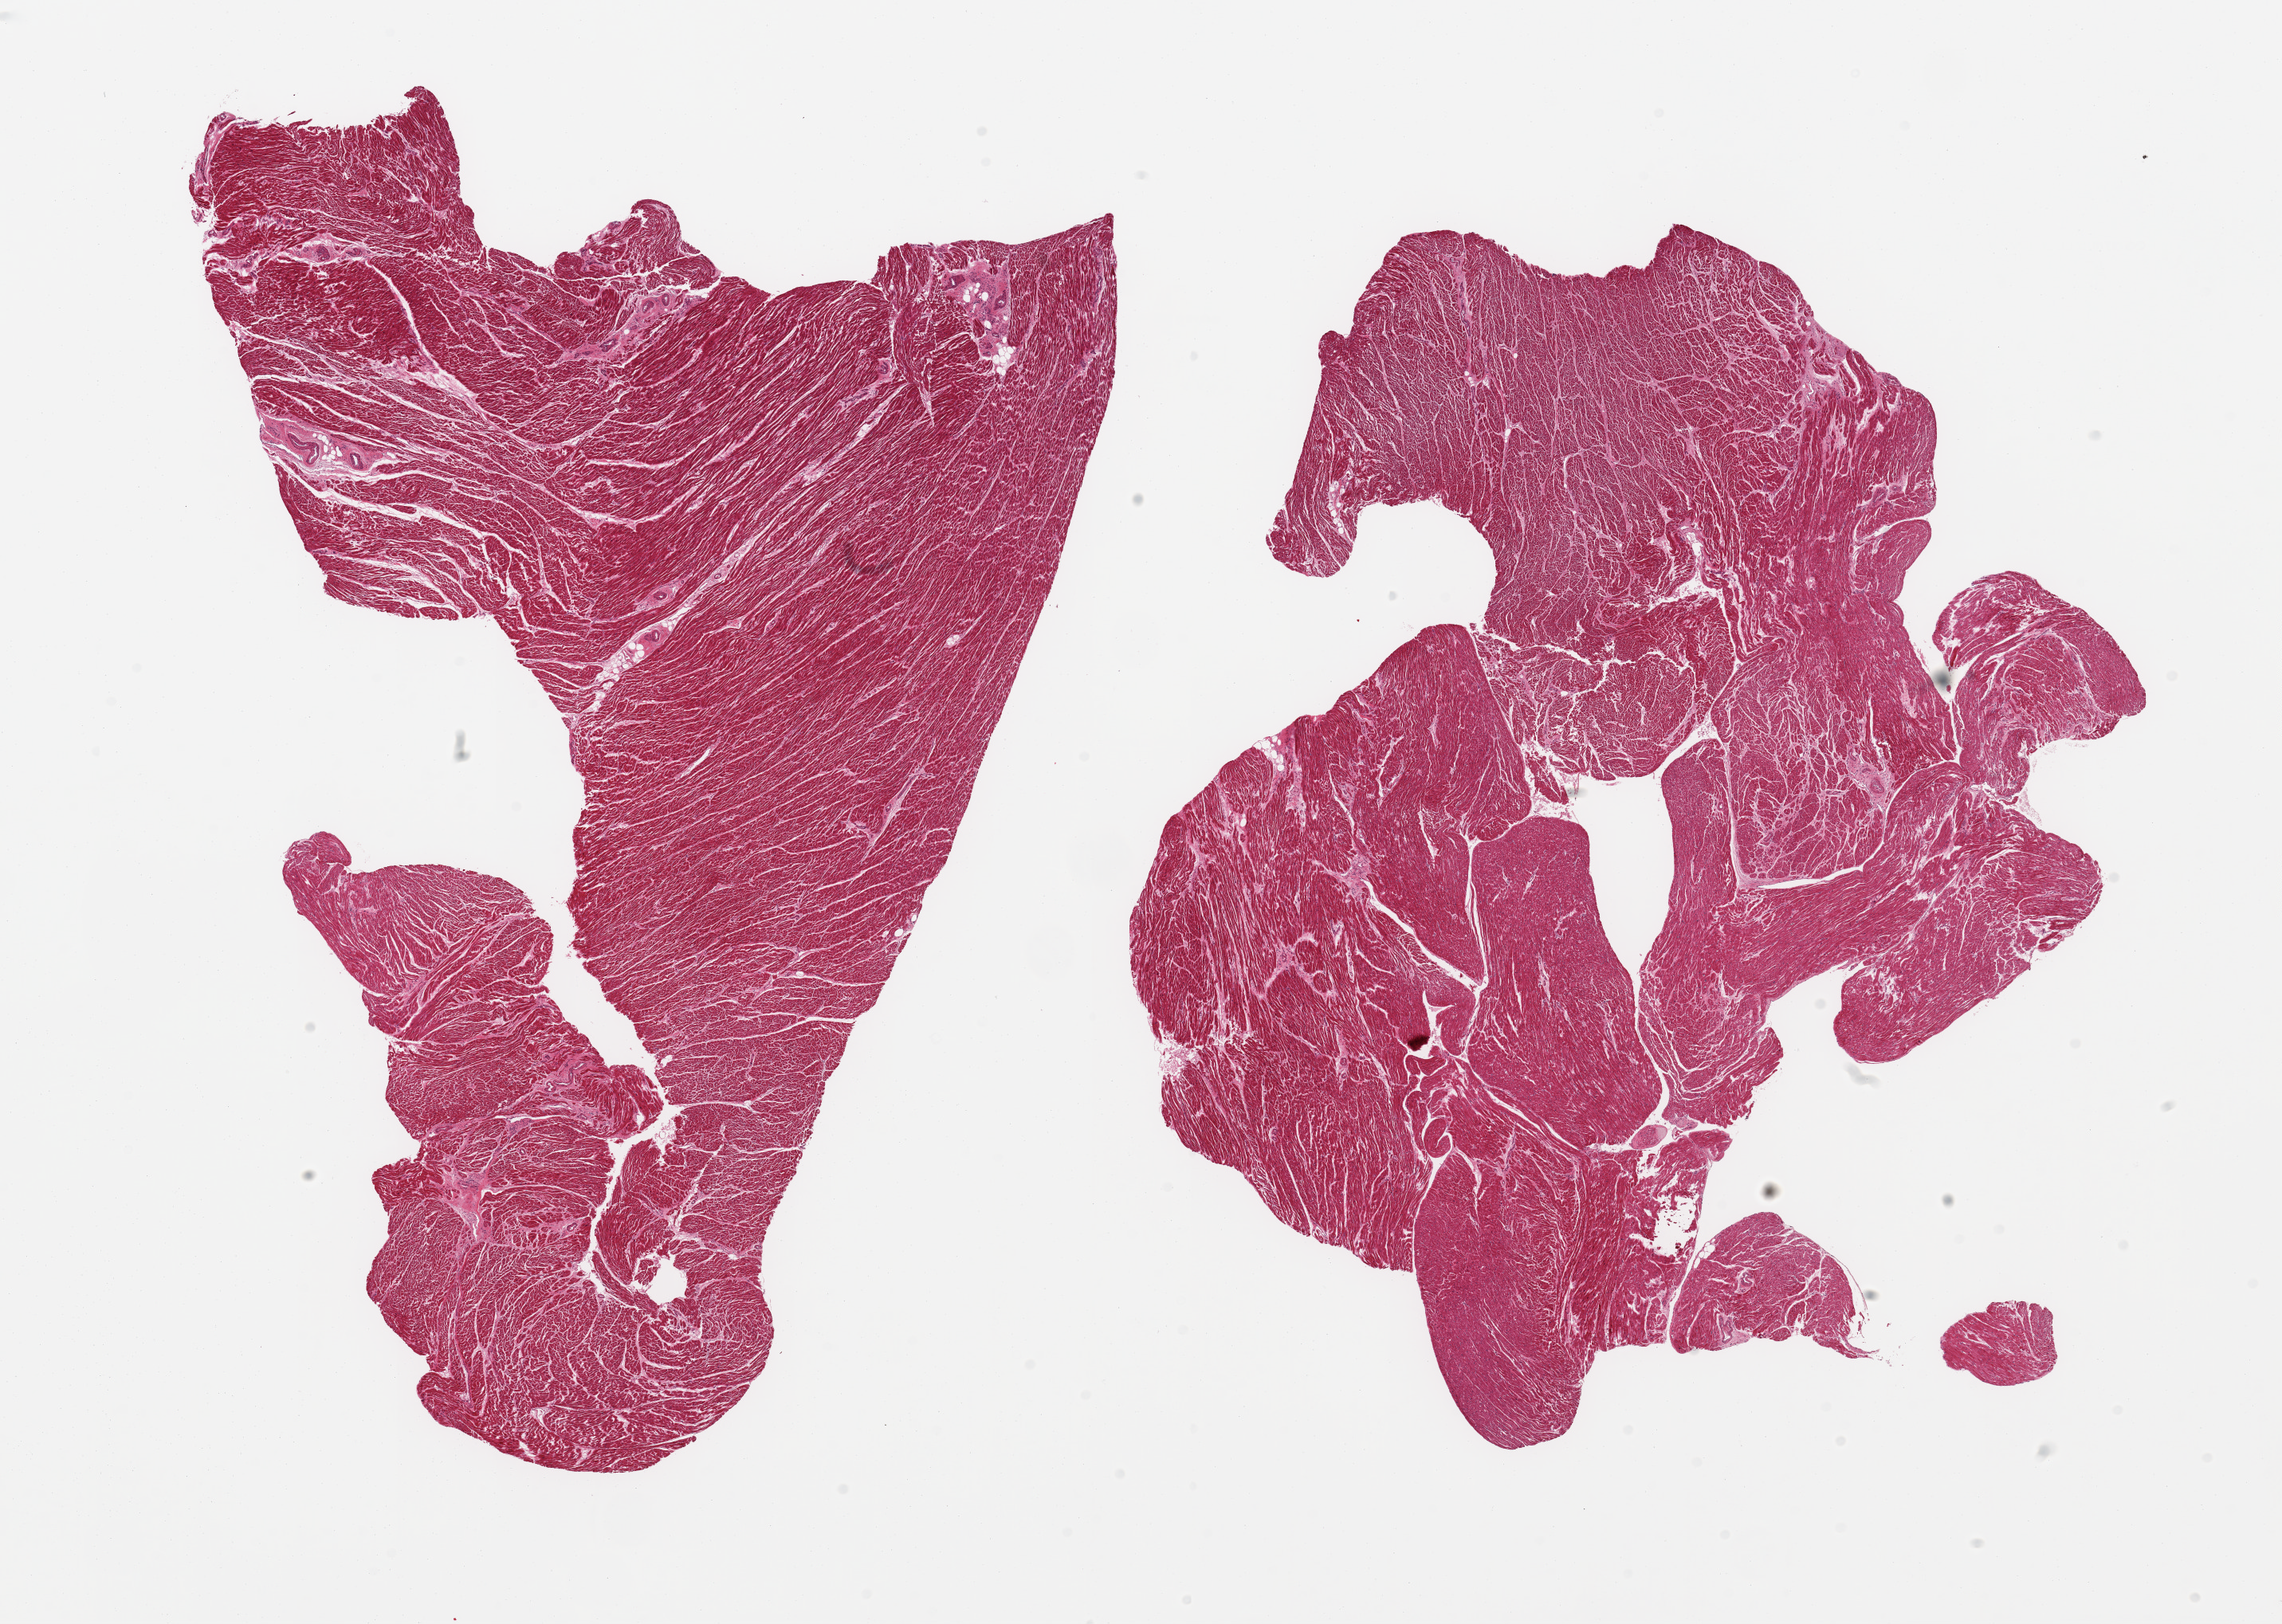
H&E whole-slide image, a low-resolution overview of the entire scanned area, about 22.6 x 16.1 mm; PAXgene-fixed paraffin-embedded (PFPE) section; sampled site (target tissue): heart; tissue donor sample. Male donor.
Reviewer comment on this tissue sample: 2 pieces, minimal interstitial fibrosis/chronic ischemic change.